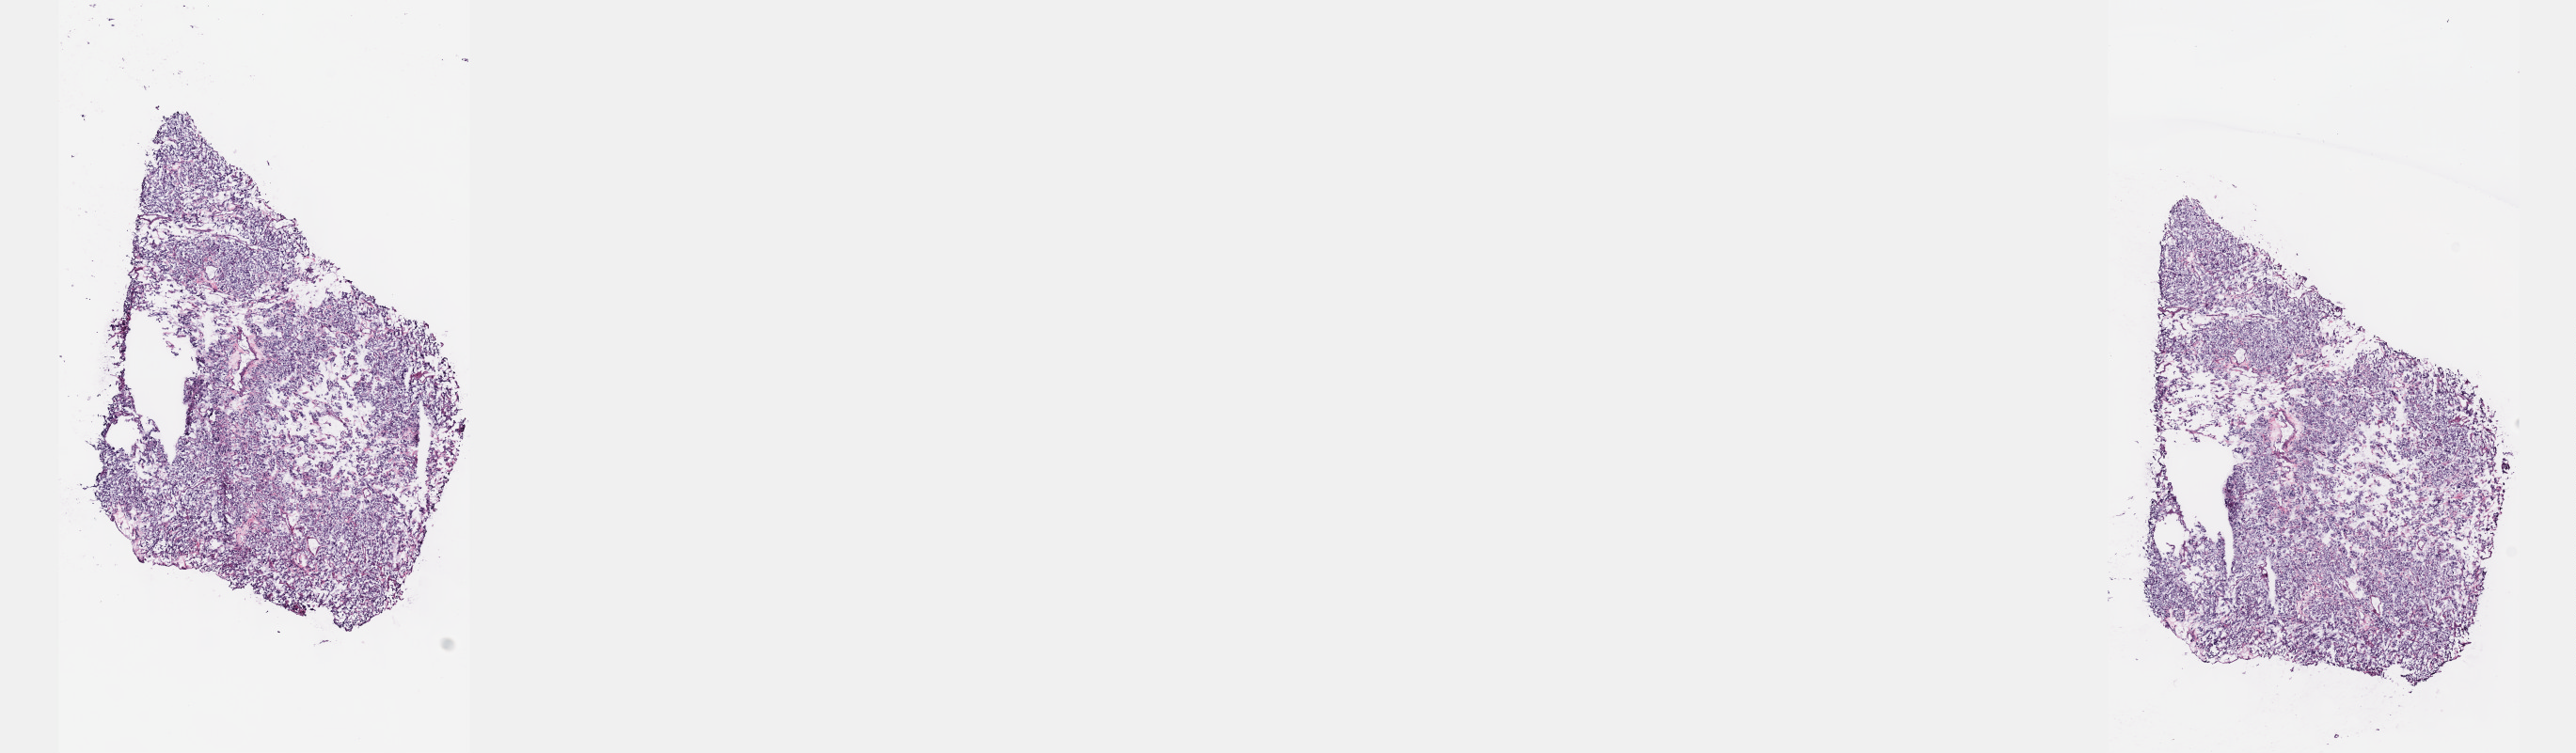
H&E-stained whole-slide image — low-resolution overview of the scanned area, about 22.1 x 6.5 mm; frozen section from the top of the tissue portion; connective, subcutaneous and other soft tissues, primary tumour sample. Female patient; age at initial diagnosis 75 years. Slide review estimates, as recorded: tumour cells 90%, tumour nuclei 90%, normal cells 0%, stromal cells 10%, necrosis 0%. Inflammatory infiltration, as recorded: lymphocyte infiltration 40%, monocyte infiltration 20%, neutrophil infiltration 20%.
Histologic diagnosis: Extra-adrenal paraganglioma, NOS.